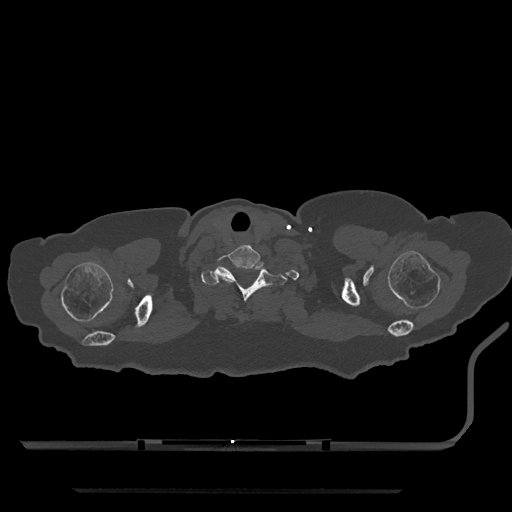
CT including the spine, one axial slice. Position 721 of 797 along the scan axis. Reconstruction kernel Br40s/3. 120 kVp. Bone window (W 1800 / L 400 HU). 0.5 mm slice thickness. 512 × 512 image matrix, field of view 440 × 440 mm. Patient: female, 51 years. Case-level facts recorded for this patient, not image findings: primary cancer: neuro; vertebrae with lytic lesions (as recorded): T8.
Annotated regions visible in this slice (semi-automatically segmented with operator editing):
- T1 vertebra: bounding box <201,262,287,302> (left, top, right, bottom; pixels)